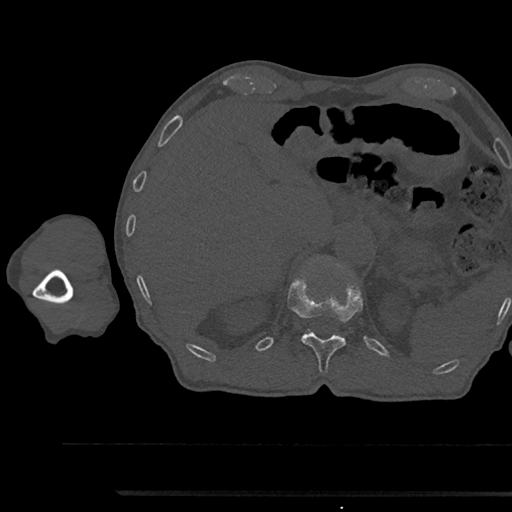
CT including the spine, one axial slice; slice 700 of 797 in the series (ordered by position); 120 kVp; bone window (W 1800 / L 400 HU); 0.5 mm slice thickness; 512 × 512 image matrix. Male patient, age 79 years. From the clinical record (not read from this slice): primary cancer: prostate.
Annotated regions visible in this slice (semi-automatically segmented with operator editing):
- T12 vertebra: box from (x=287, y=279) to (x=362, y=372) px